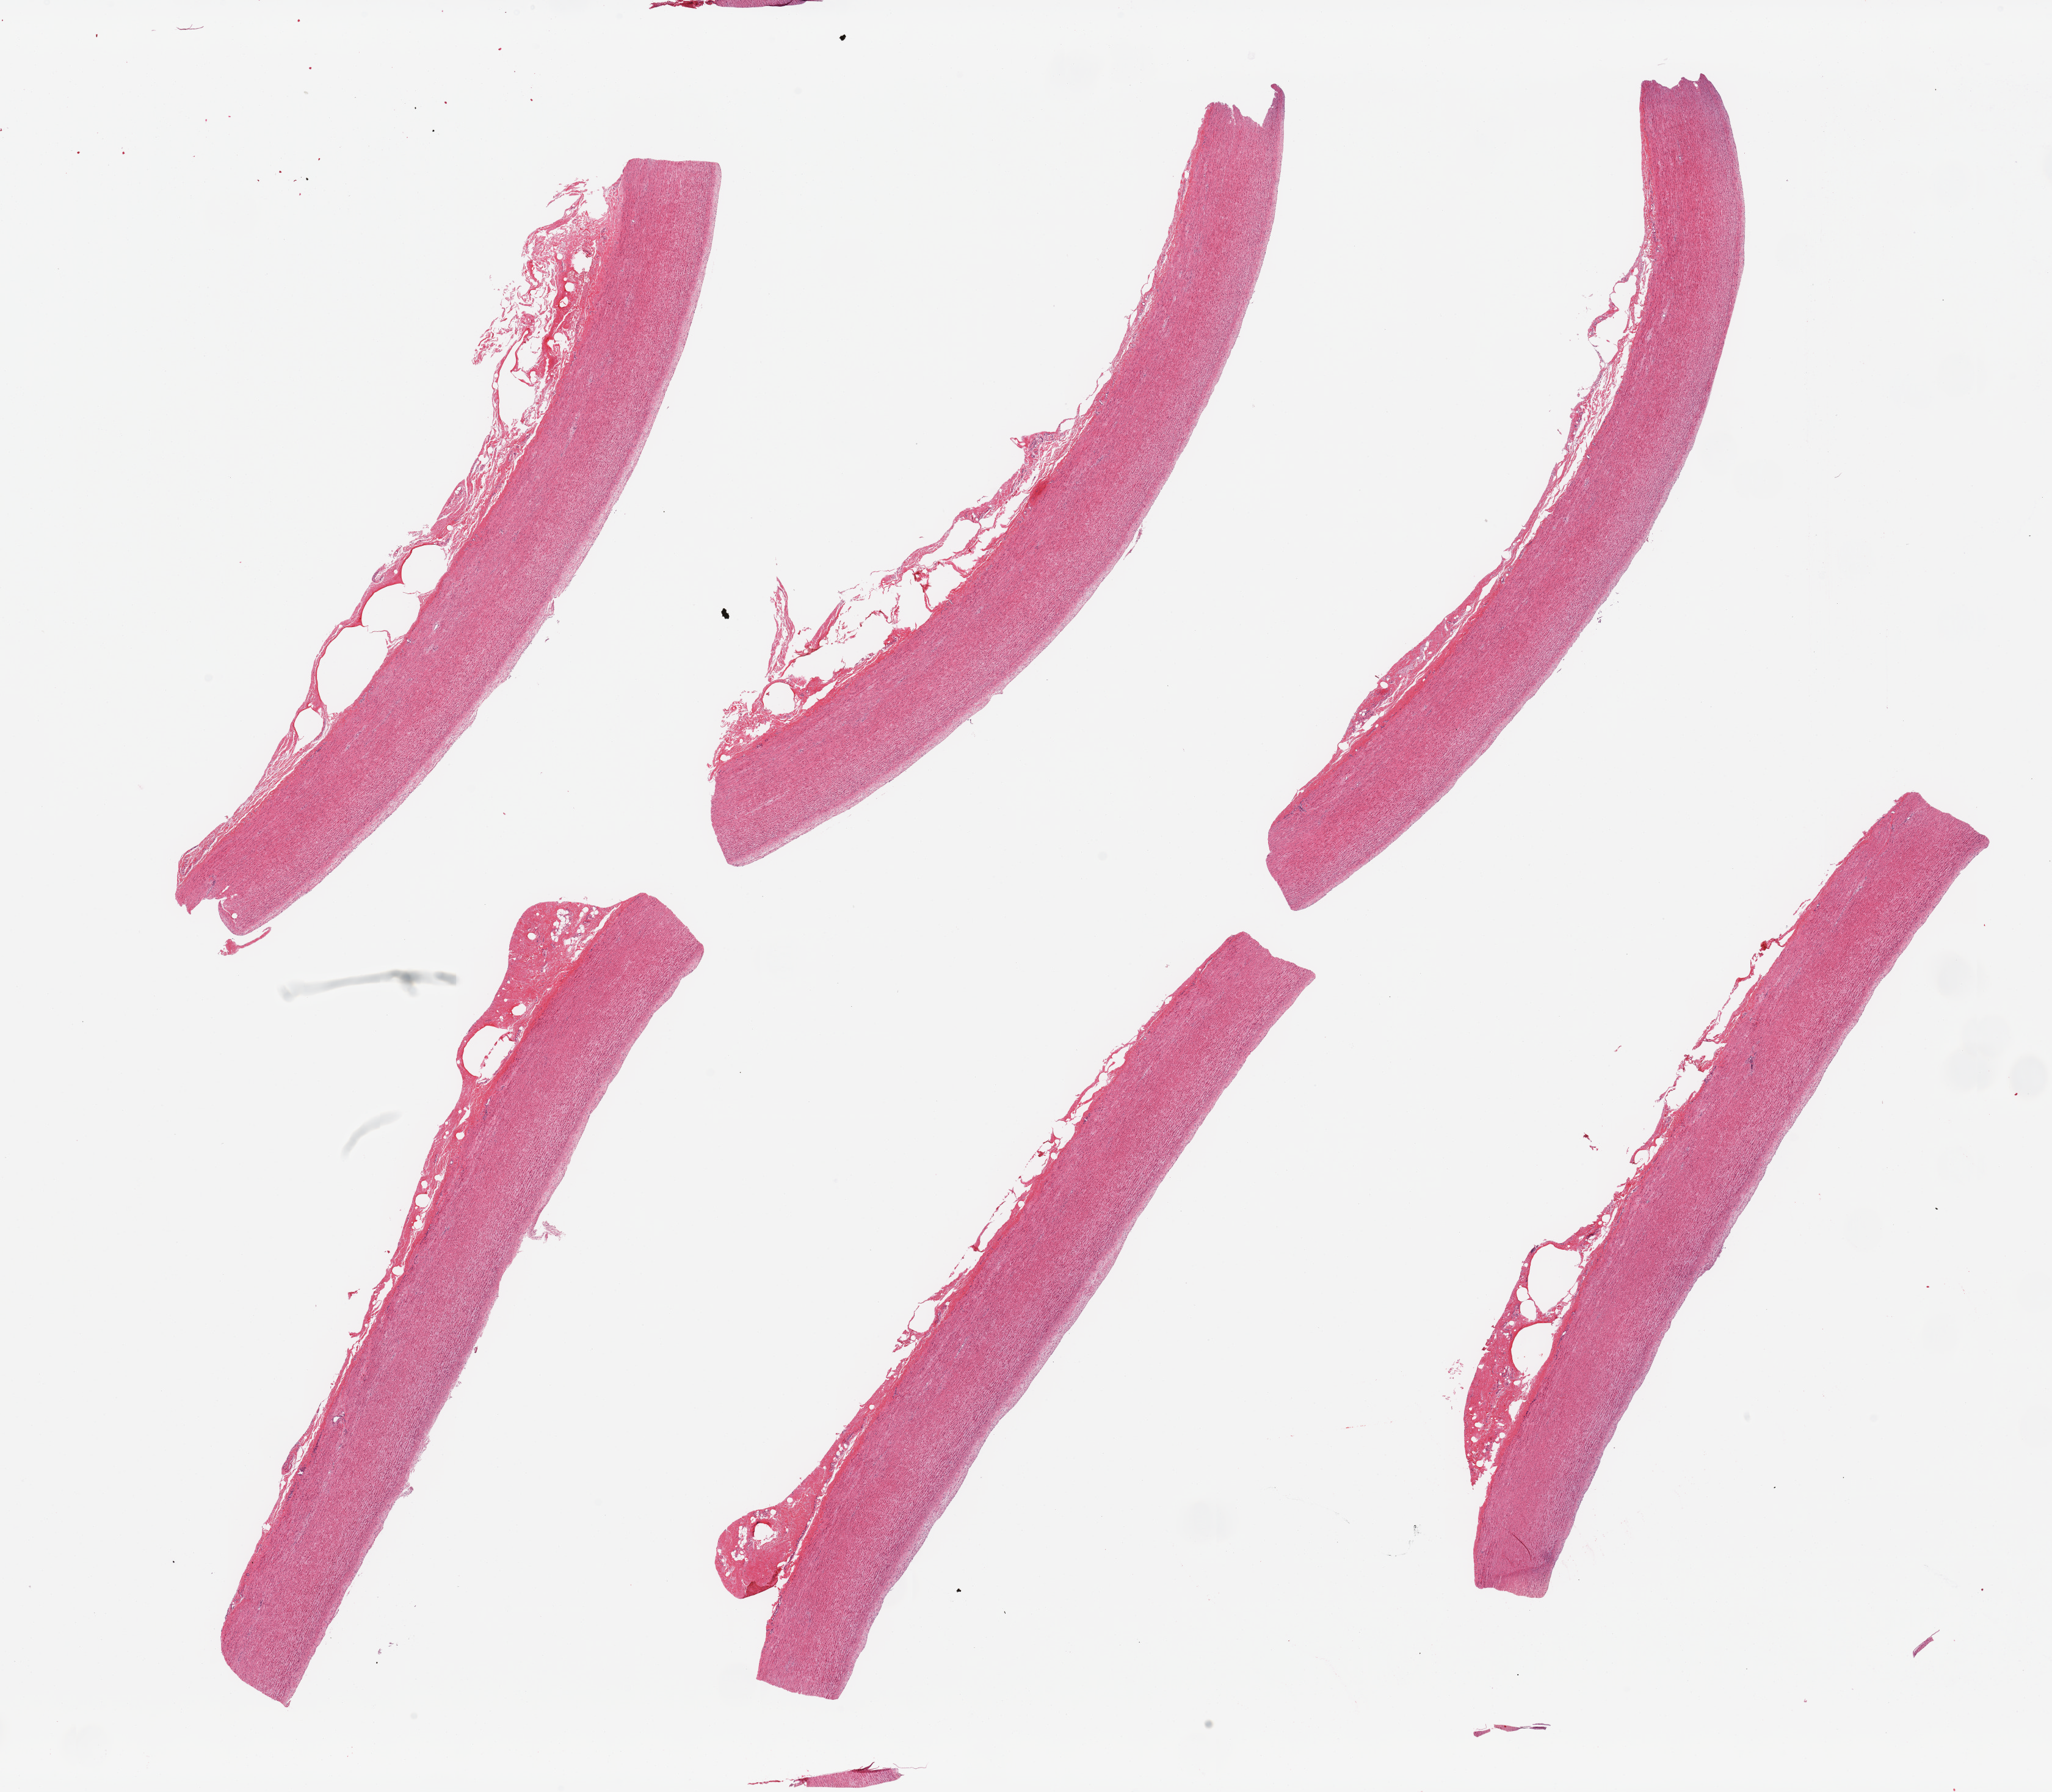
Whole-slide image, hematoxylin and eosin (H&E) stain, brightfield — a low-resolution overview of the entire scanned area, about 26.6 x 23.2 mm. PAXgene-fixed, paraffin-embedded tissue. Target tissue: aorta. Donor tissue sample. Male donor.
Pathologist's review note for this sample: 6 pieces, trace atherosis.